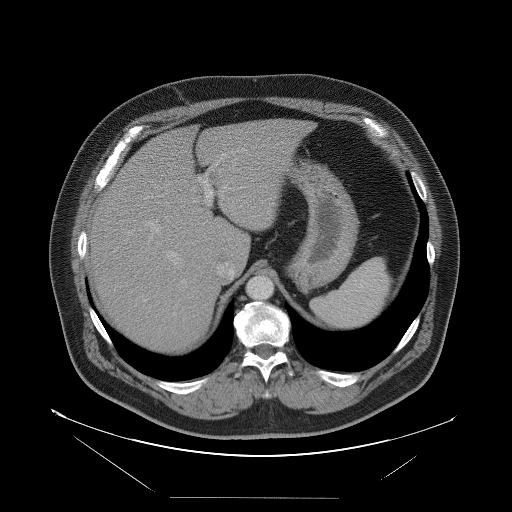
Contrast-enhanced abdominal CT, one axial slice; position 73 of 114 along the scan axis; soft-tissue window (W 400 / L 40 HU); 5 mm slice thickness; 512 × 512 image matrix, field of view 500 × 500 mm. Male patient, age 61 years. From the clinical record (not read from this slice): diagnosis: colorectal cancer liver metastases, imaged before liver resection; multiple liver metastases: no; largest metastasis: 6.5 cm; disease in both lobes: yes.
Outlined on this slice (expert manual segmentation):
- hepatic veins: bounding box <159,164,249,286> (left, top, right, bottom; pixels)
- liver: <89,120,309,353>
- planned liver remnant (the part of the liver to remain after resection): <146,120,309,265>
- portal vein (with intrahepatic branches): <142,148,247,302>